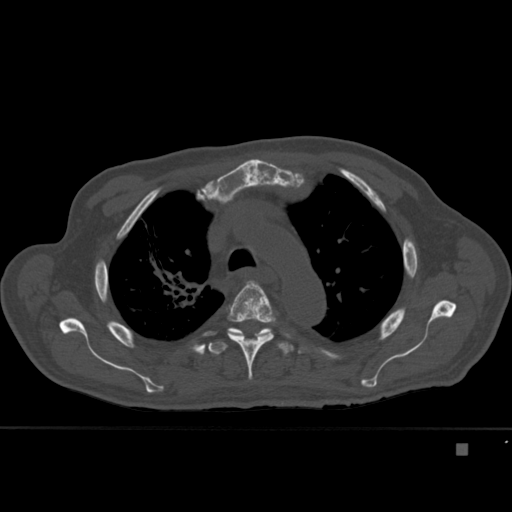
CT including the spine, one axial slice; slice 318 of 451 in the series (ordered by position); bone window (W 1800 / L 400 HU); 1.5 mm slice thickness; 512 × 512 image matrix. Male patient, age 75 years. Case-level facts recorded for this patient, not image findings: primary cancer: prostate.
Outlined on this slice (semi-automatic segmentation, software-assisted and operator-edited):
- T3 vertebra: bounding box [x1, y1, x2, y2] px = [254, 331, 270, 335]
- T4 vertebra: [227, 280, 276, 380]
- T5 vertebra: [208, 328, 294, 355]